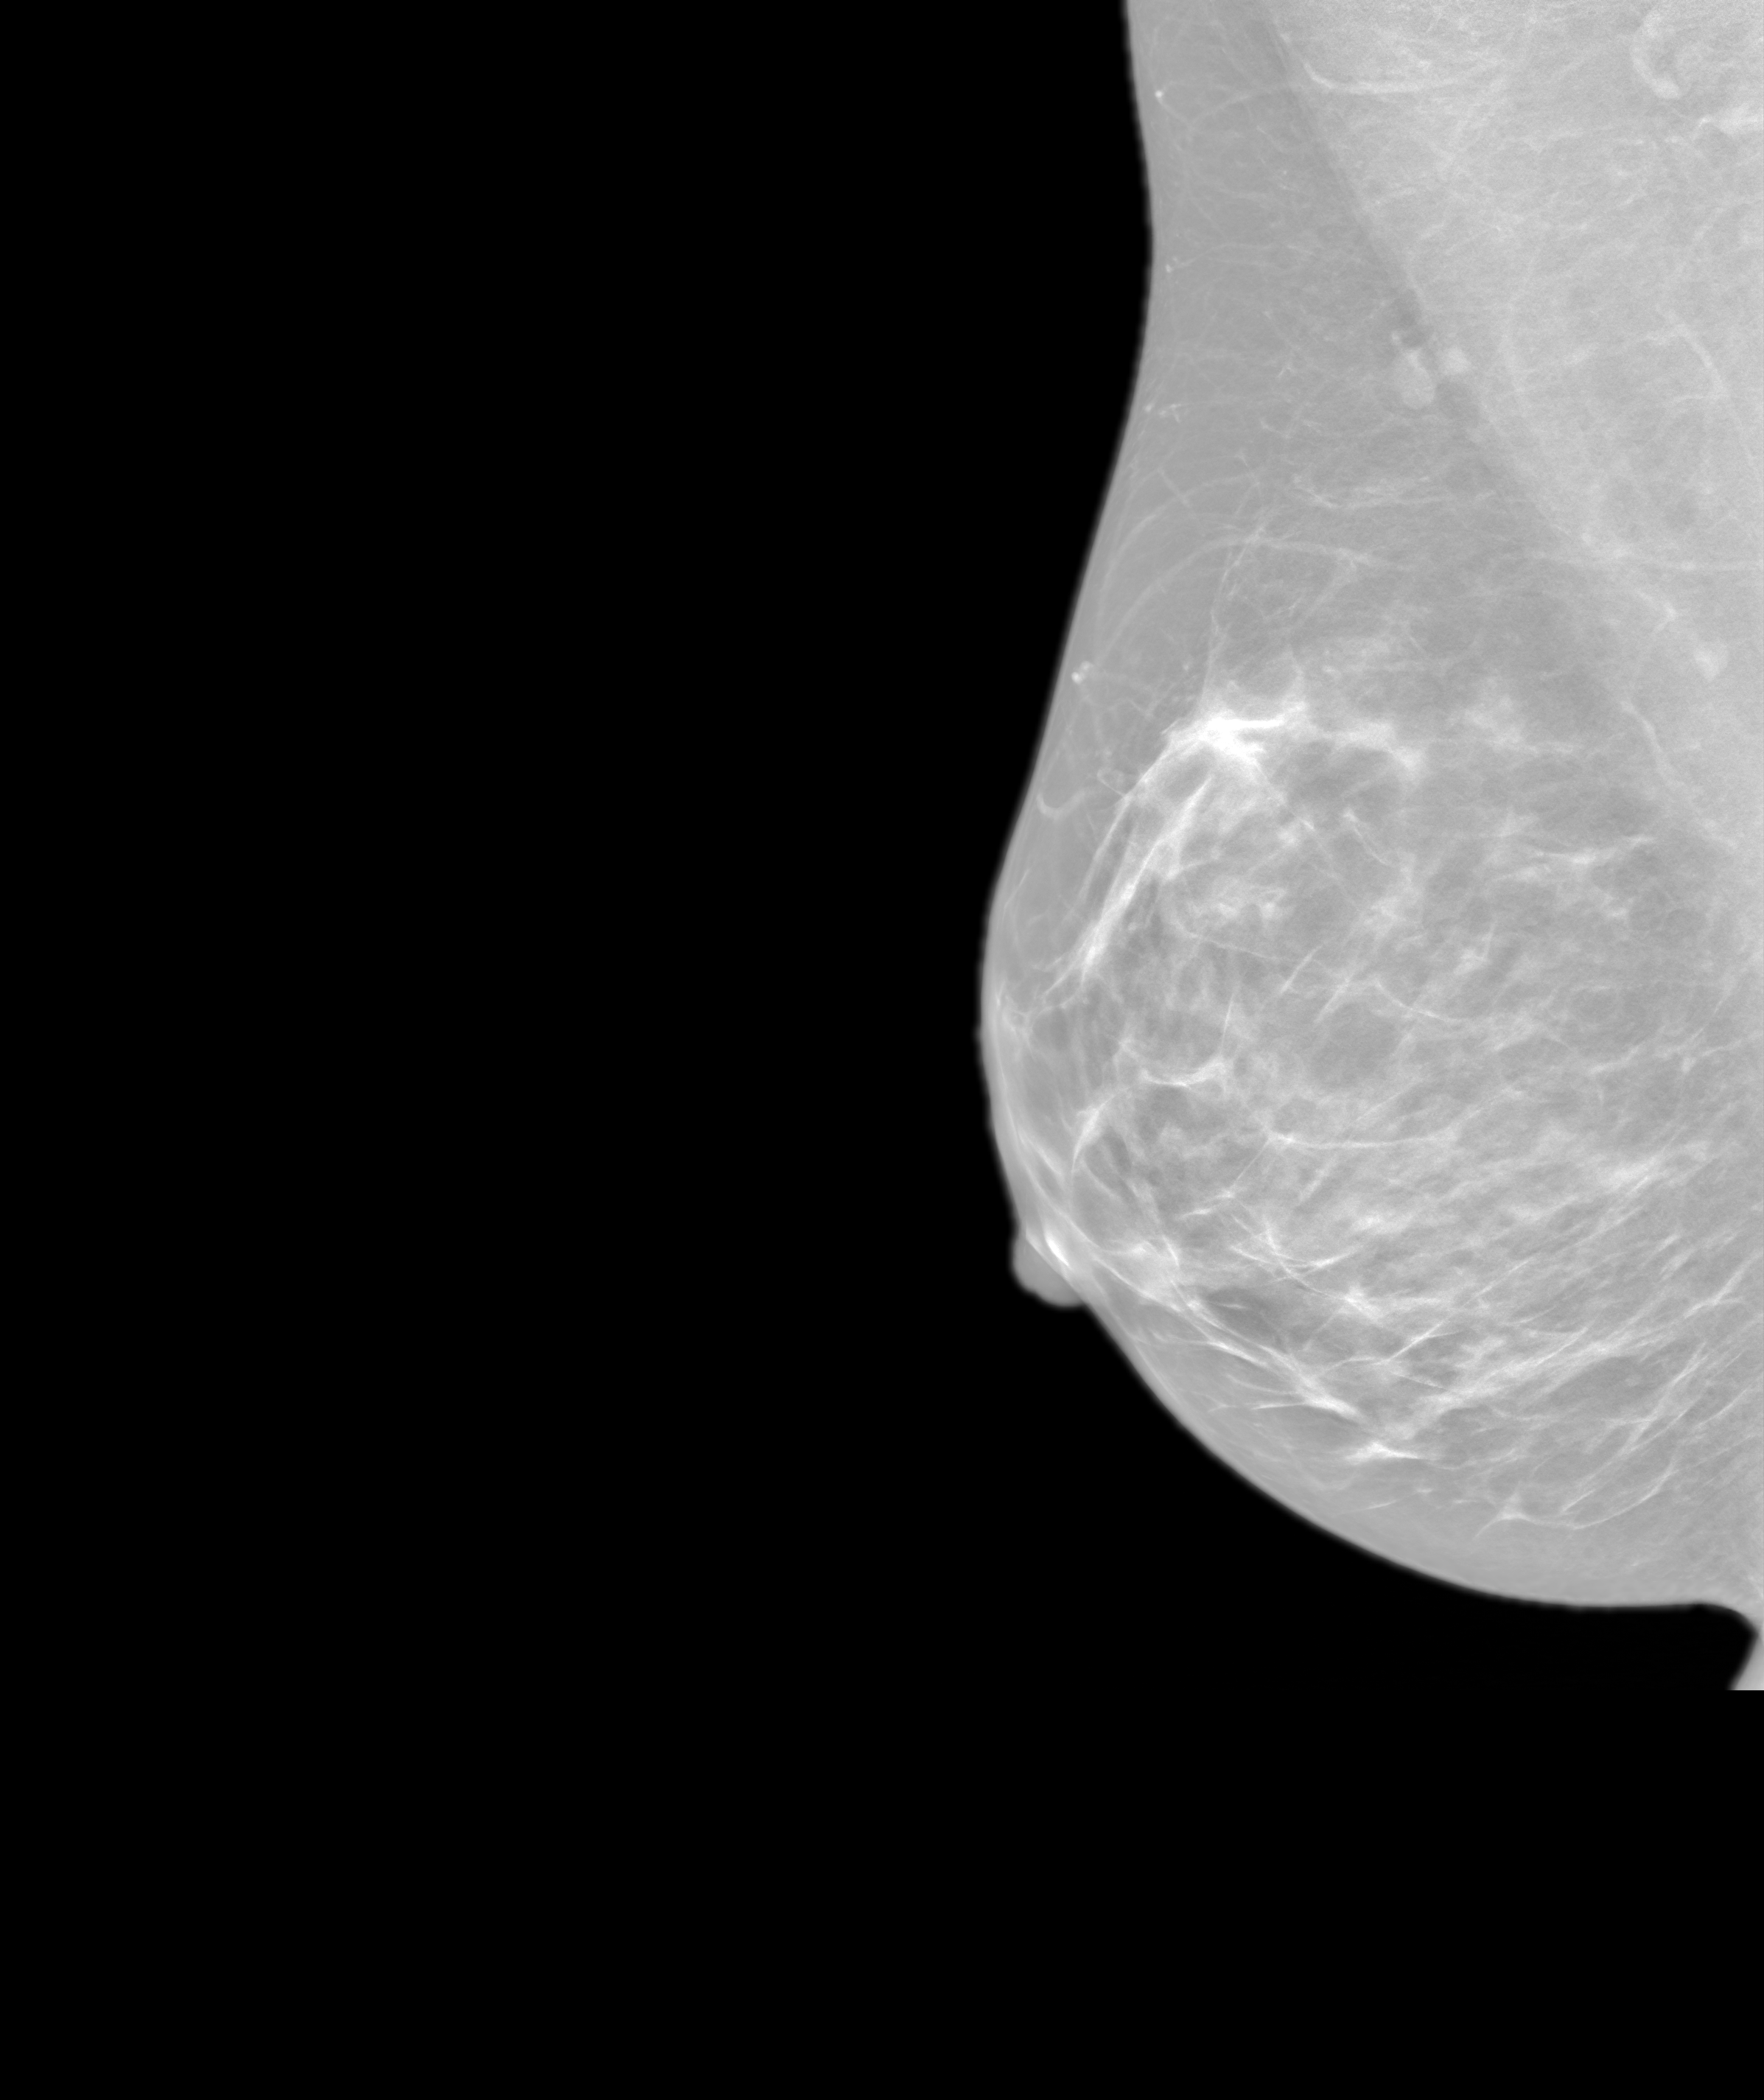
Annual screening mammography examination, system: SenoIris_1SP2(440). Patient aged 46 years (female).
Image type: synthesized 2-D view from tomosynthesis. Breast: right. Projection: MLO view.